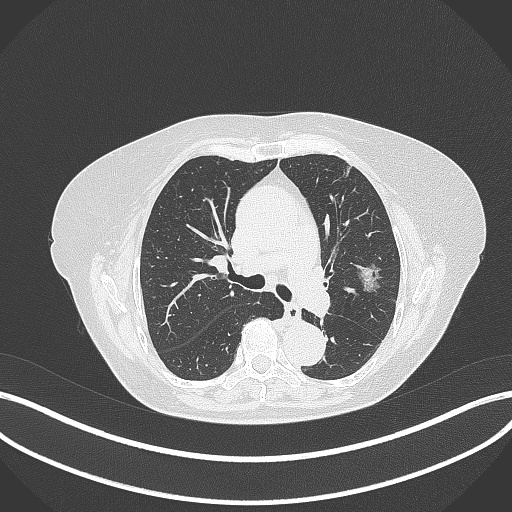
Chest CT, one axial slice; position 205 of 316 along the scan axis; 120 kVp; lung window (W 1500 / L -600 HU); 1 mm slice thickness; 512 × 512 image matrix. Patient: female, 75 years. Case-level facts recorded for this patient, not image findings: clinical TNM (as recorded): T1c N0 M0.
Outlined on this slice (rectangle marked by the reading radiologist):
- lung tumour (recorded histology: adenocarcinoma): bounding box (x1, y1, x2, y2) in pixels: (353, 263, 384, 295)